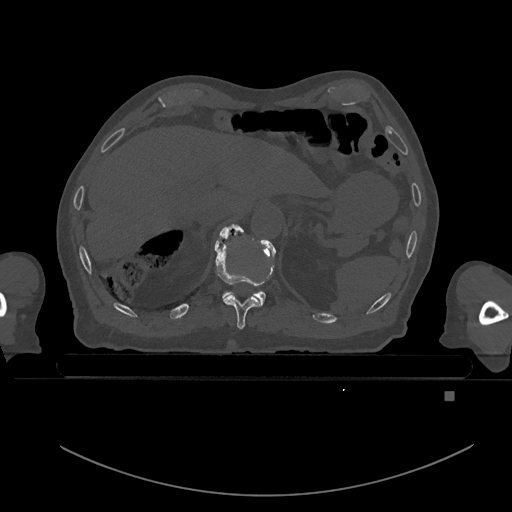
CT including the spine, one axial slice; slice 66 of 969 in the series (ordered by position); bone window (W 1800 / L 400 HU); 0.5 mm slice thickness; 512 × 512 image matrix, field of view 456 × 456 mm. Patient: male, 82 years. From the clinical record (not read from this slice): primary cancer: prostate; vertebrae with lytic lesions (as recorded): T11, T9, T8, T2.
Structures marked on this image (semi-automatic segmentation, software-assisted and operator-edited):
- T10 vertebra: box from (x=214, y=224) to (x=261, y=330) px
- T11 vertebra: (x=219, y=223)–(x=275, y=306)